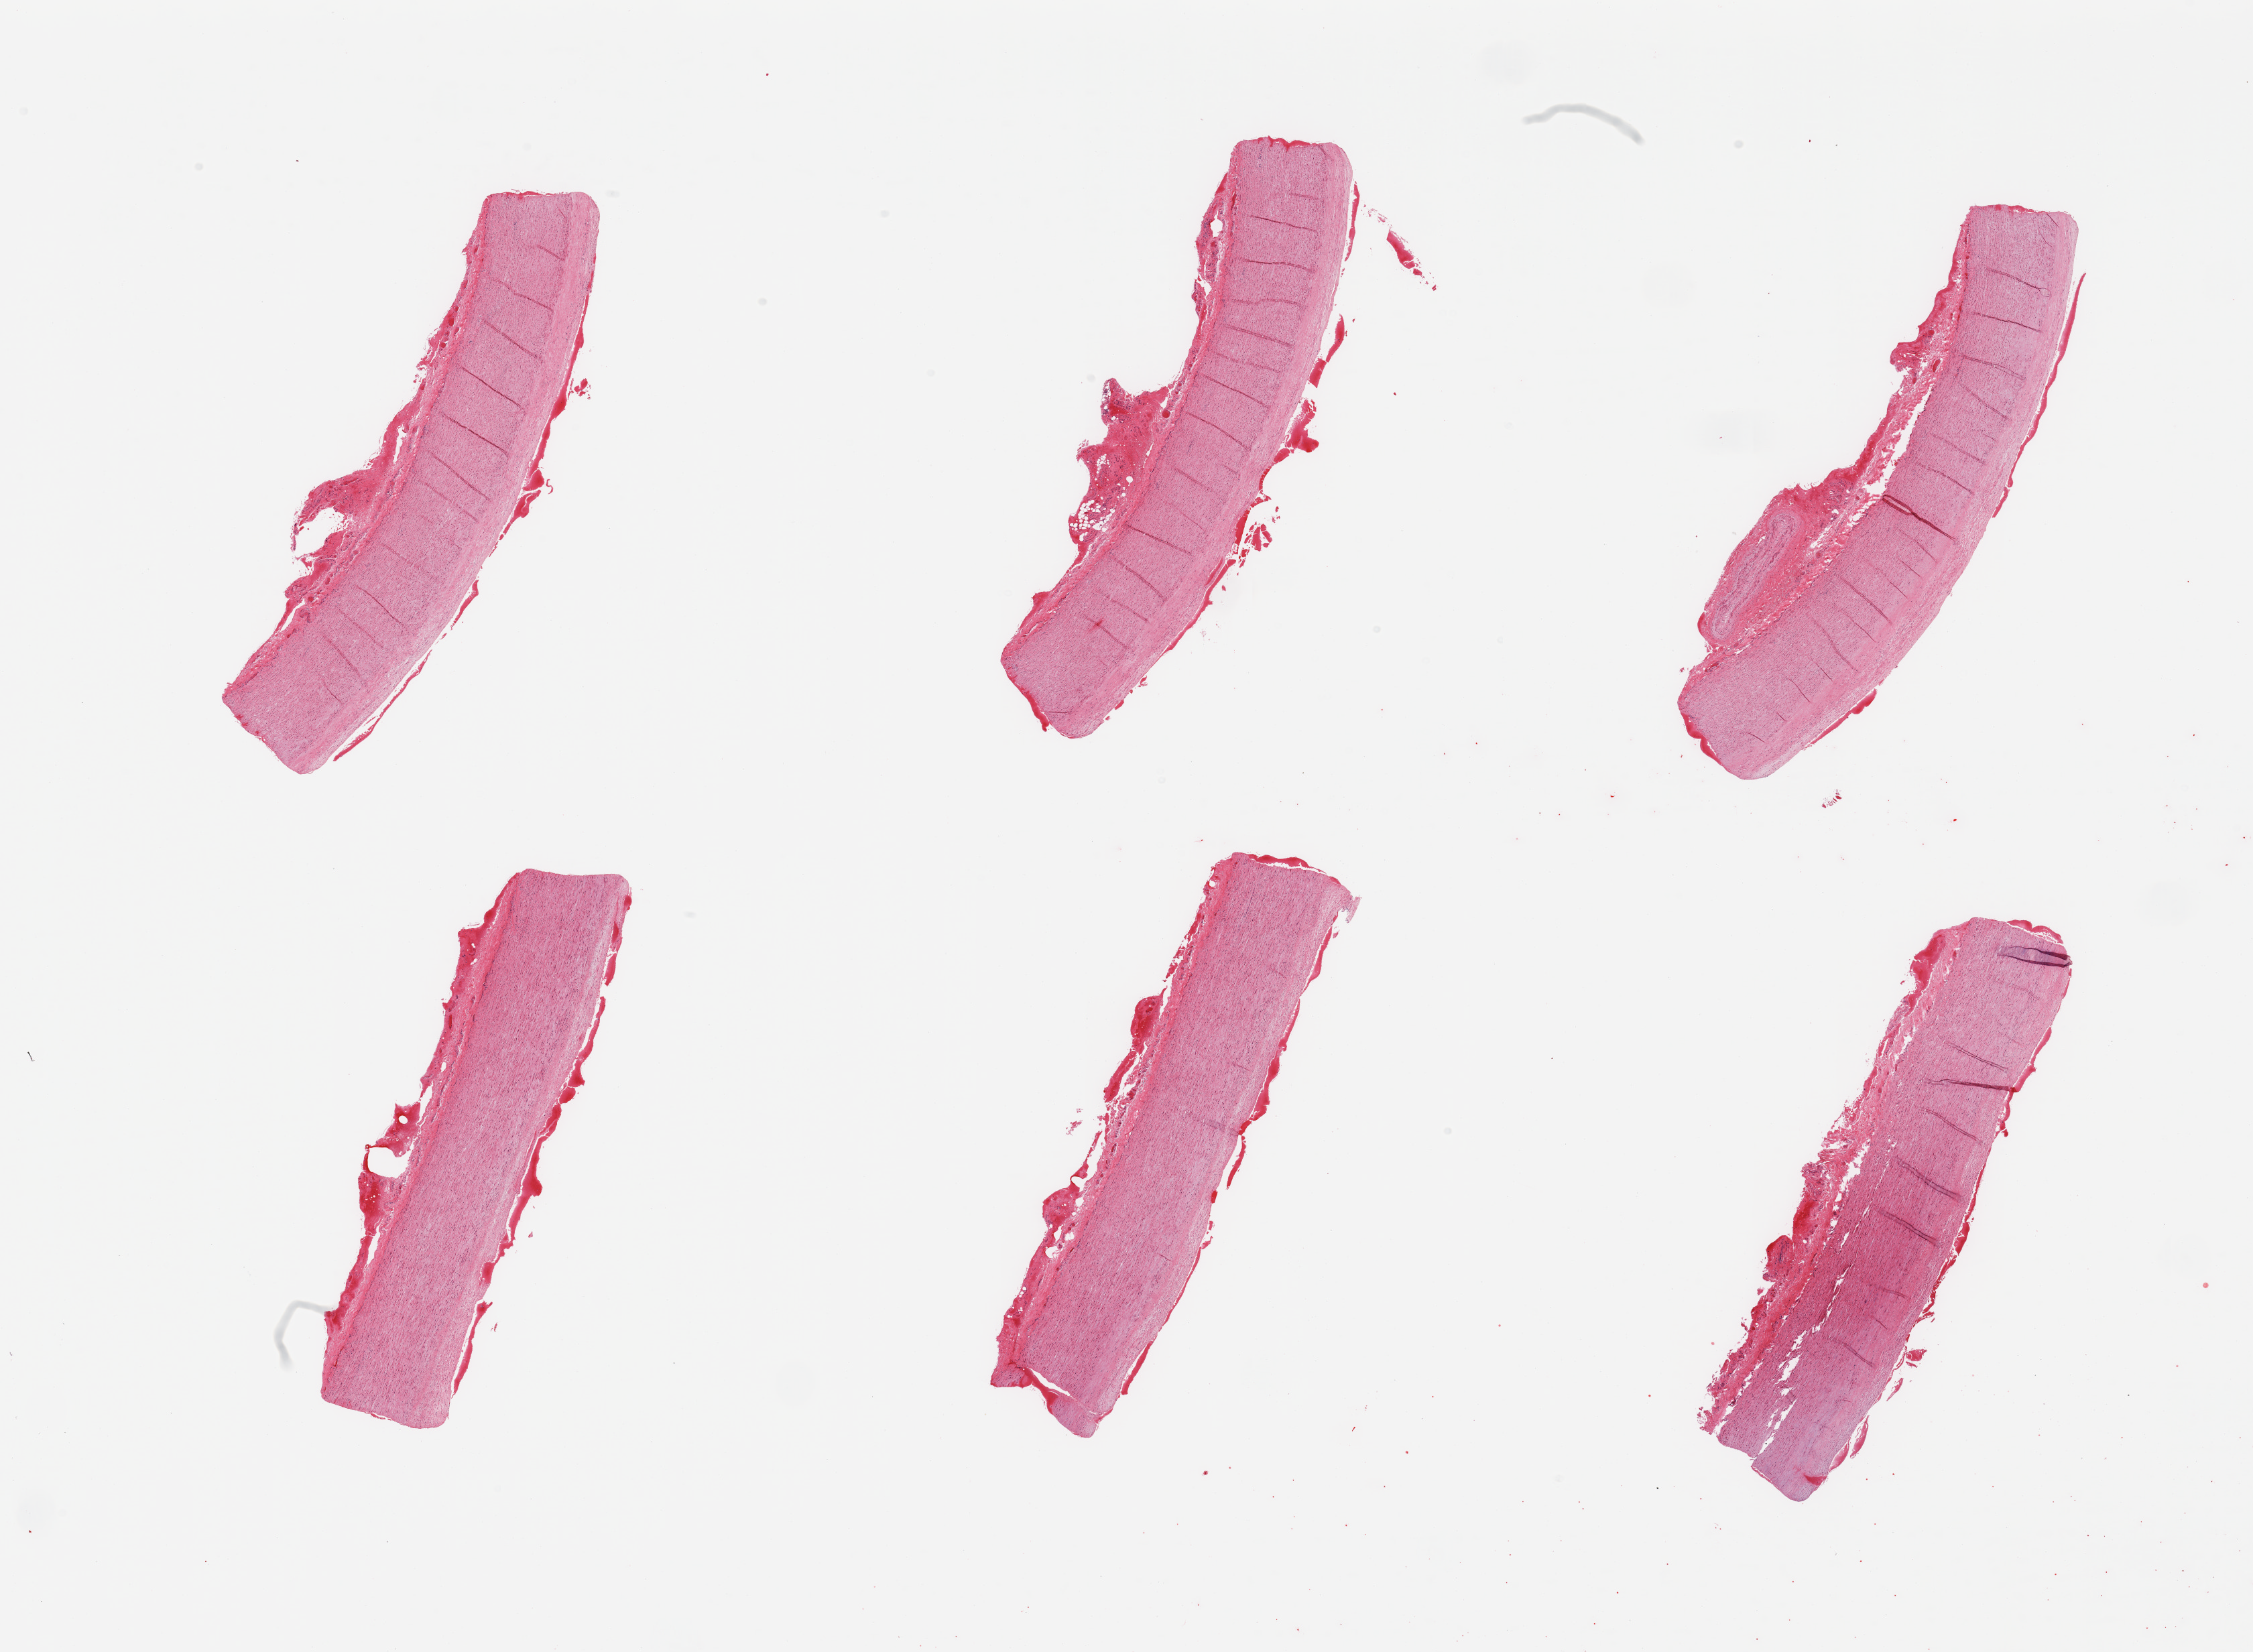
Hematoxylin and eosin (H&E) whole-slide image, brightfield — shown as a low-resolution overview of the whole scanned area (about 26.6 x 19.5 mm). PAXgene-fixed paraffin-embedded (PFPE) section. Sampled site (target tissue): aorta. Tissue donor sample. Female donor.
Review note (as recorded): 6 pieces; thin fibrous plaques; blood on both surfaces.